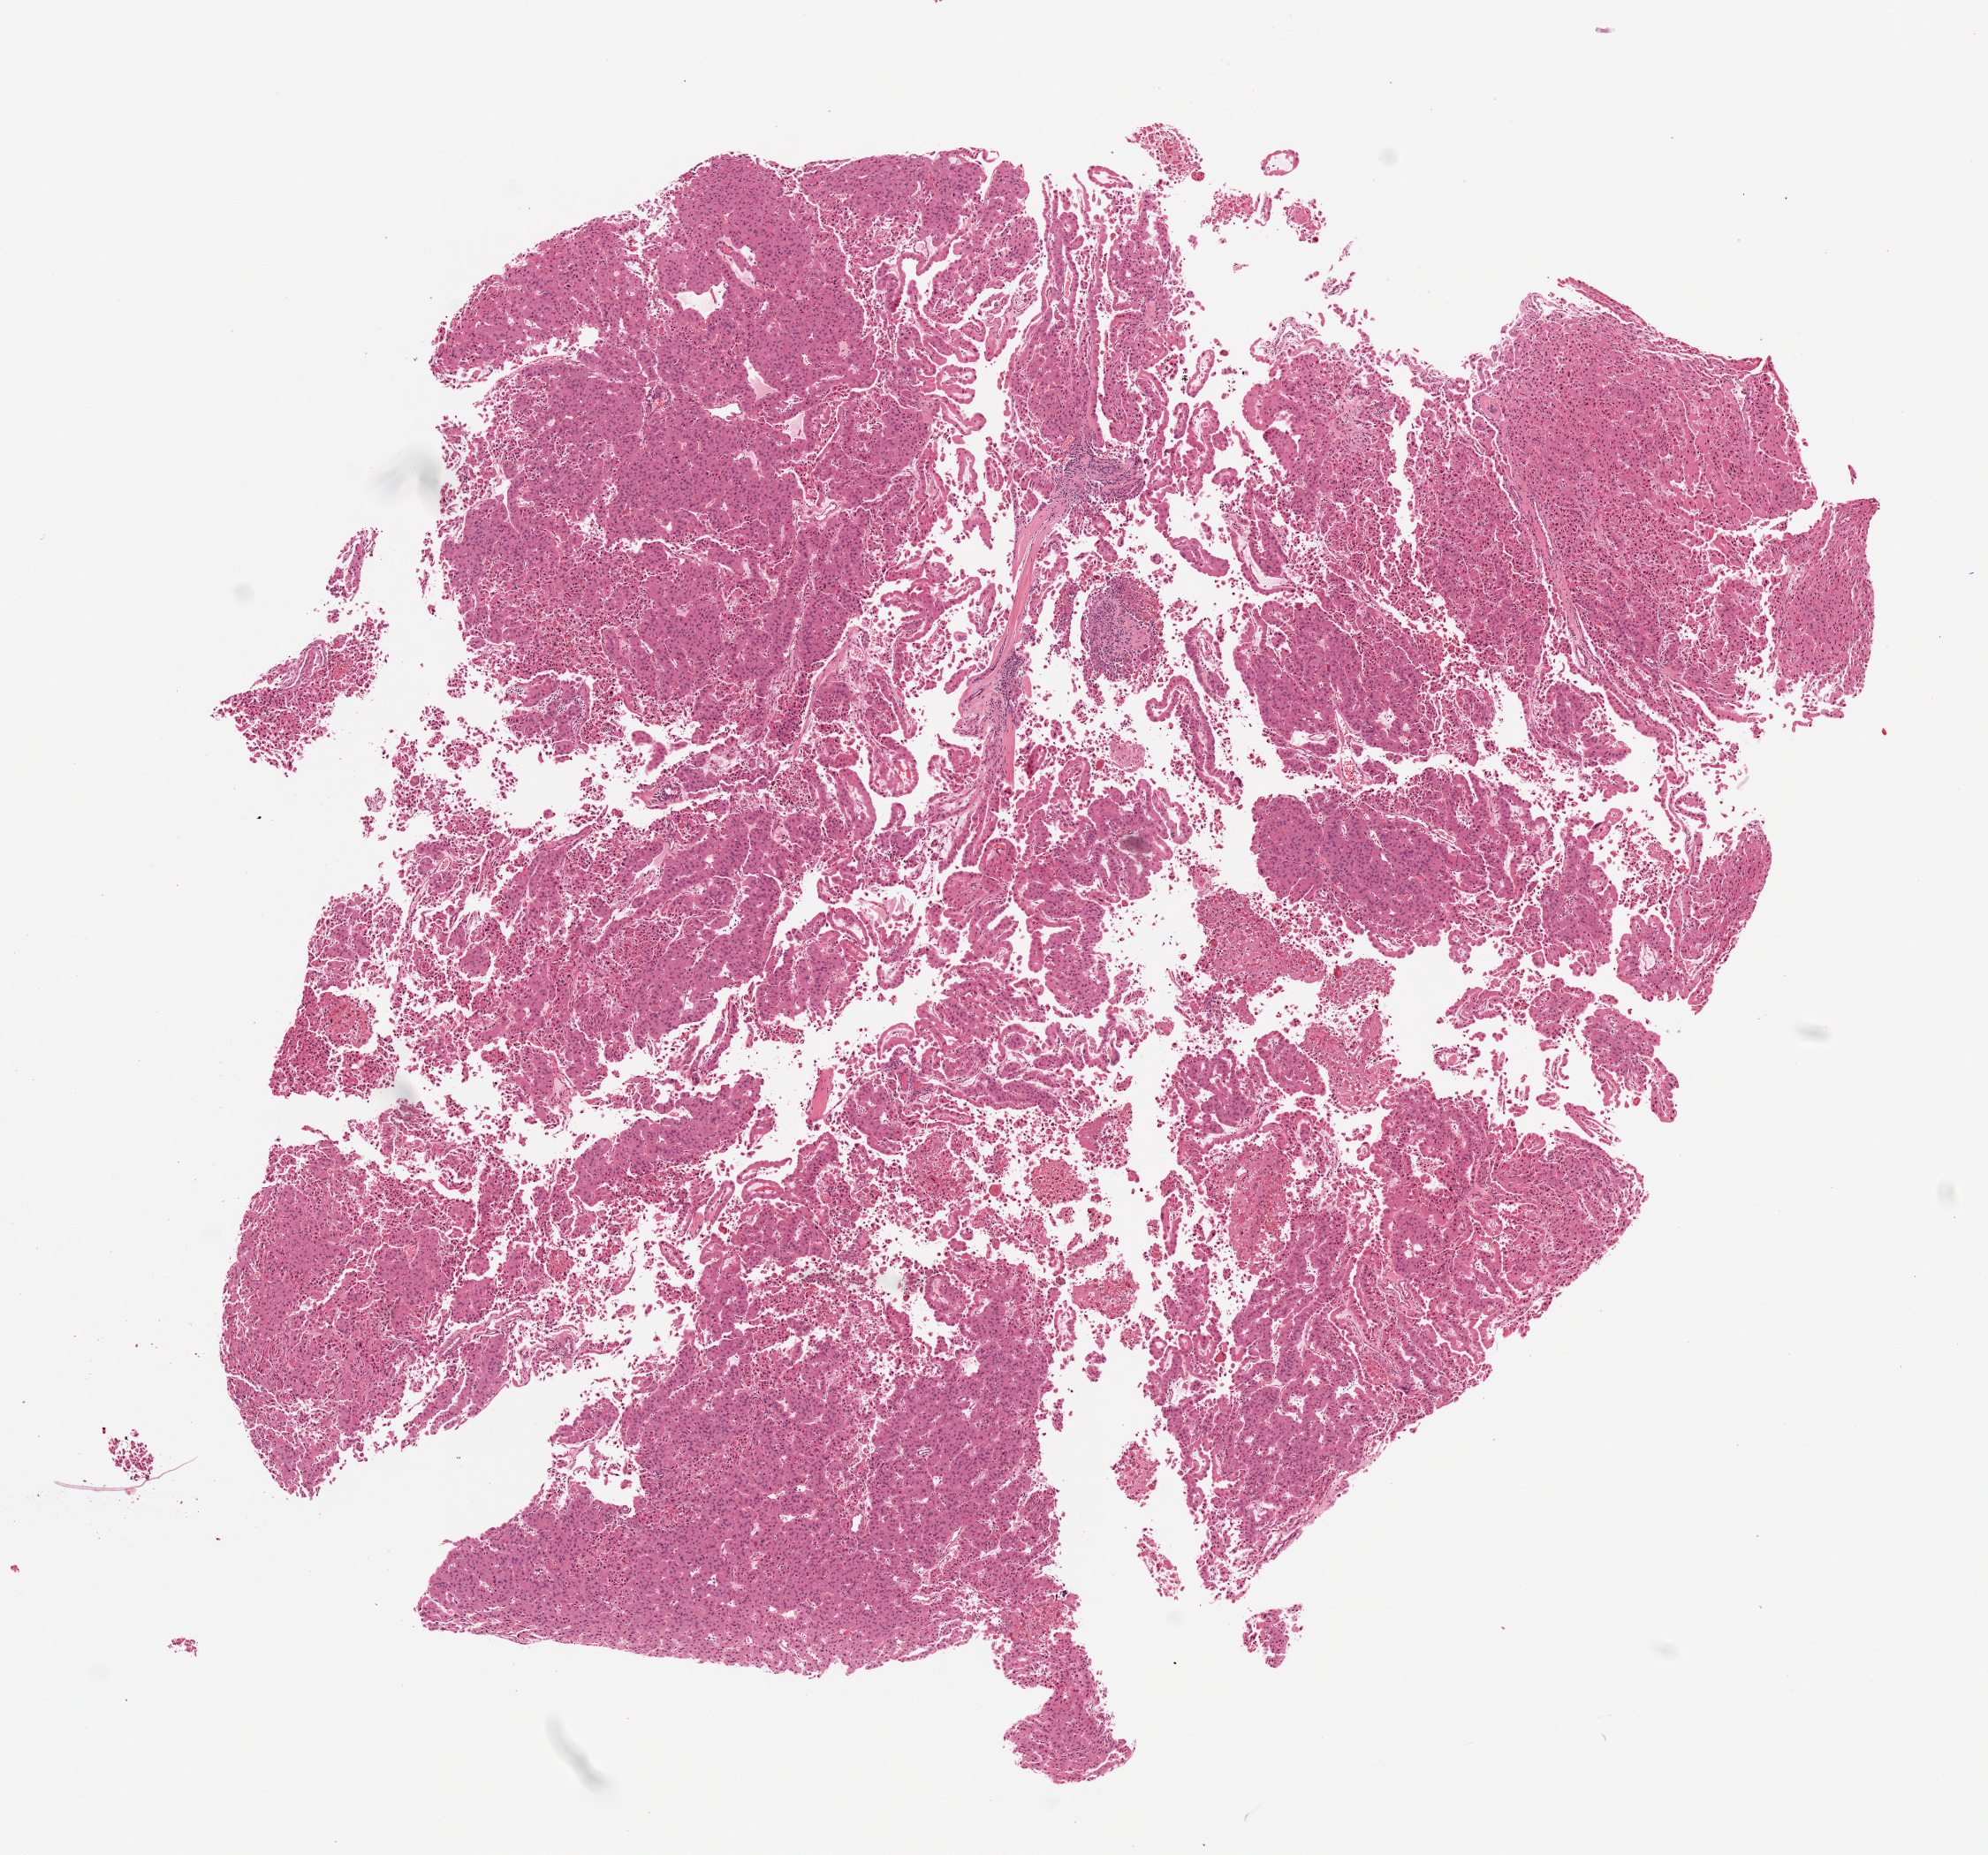
Whole-slide histology image, Hematoxylin and eosin (H&E) stained — whole scanned area (about 9.0 x 8.4 mm) shown as a low-resolution overview. Formalin-fixed paraffin-embedded (FFPE) diagnostic section. Primary tumour sample from the thyroid. Male, age 36 years at initial diagnosis.
- AJCC pathologic stage: I
- pathologic diagnosis: Papillary carcinoma, follicular variant (thyroid gland)